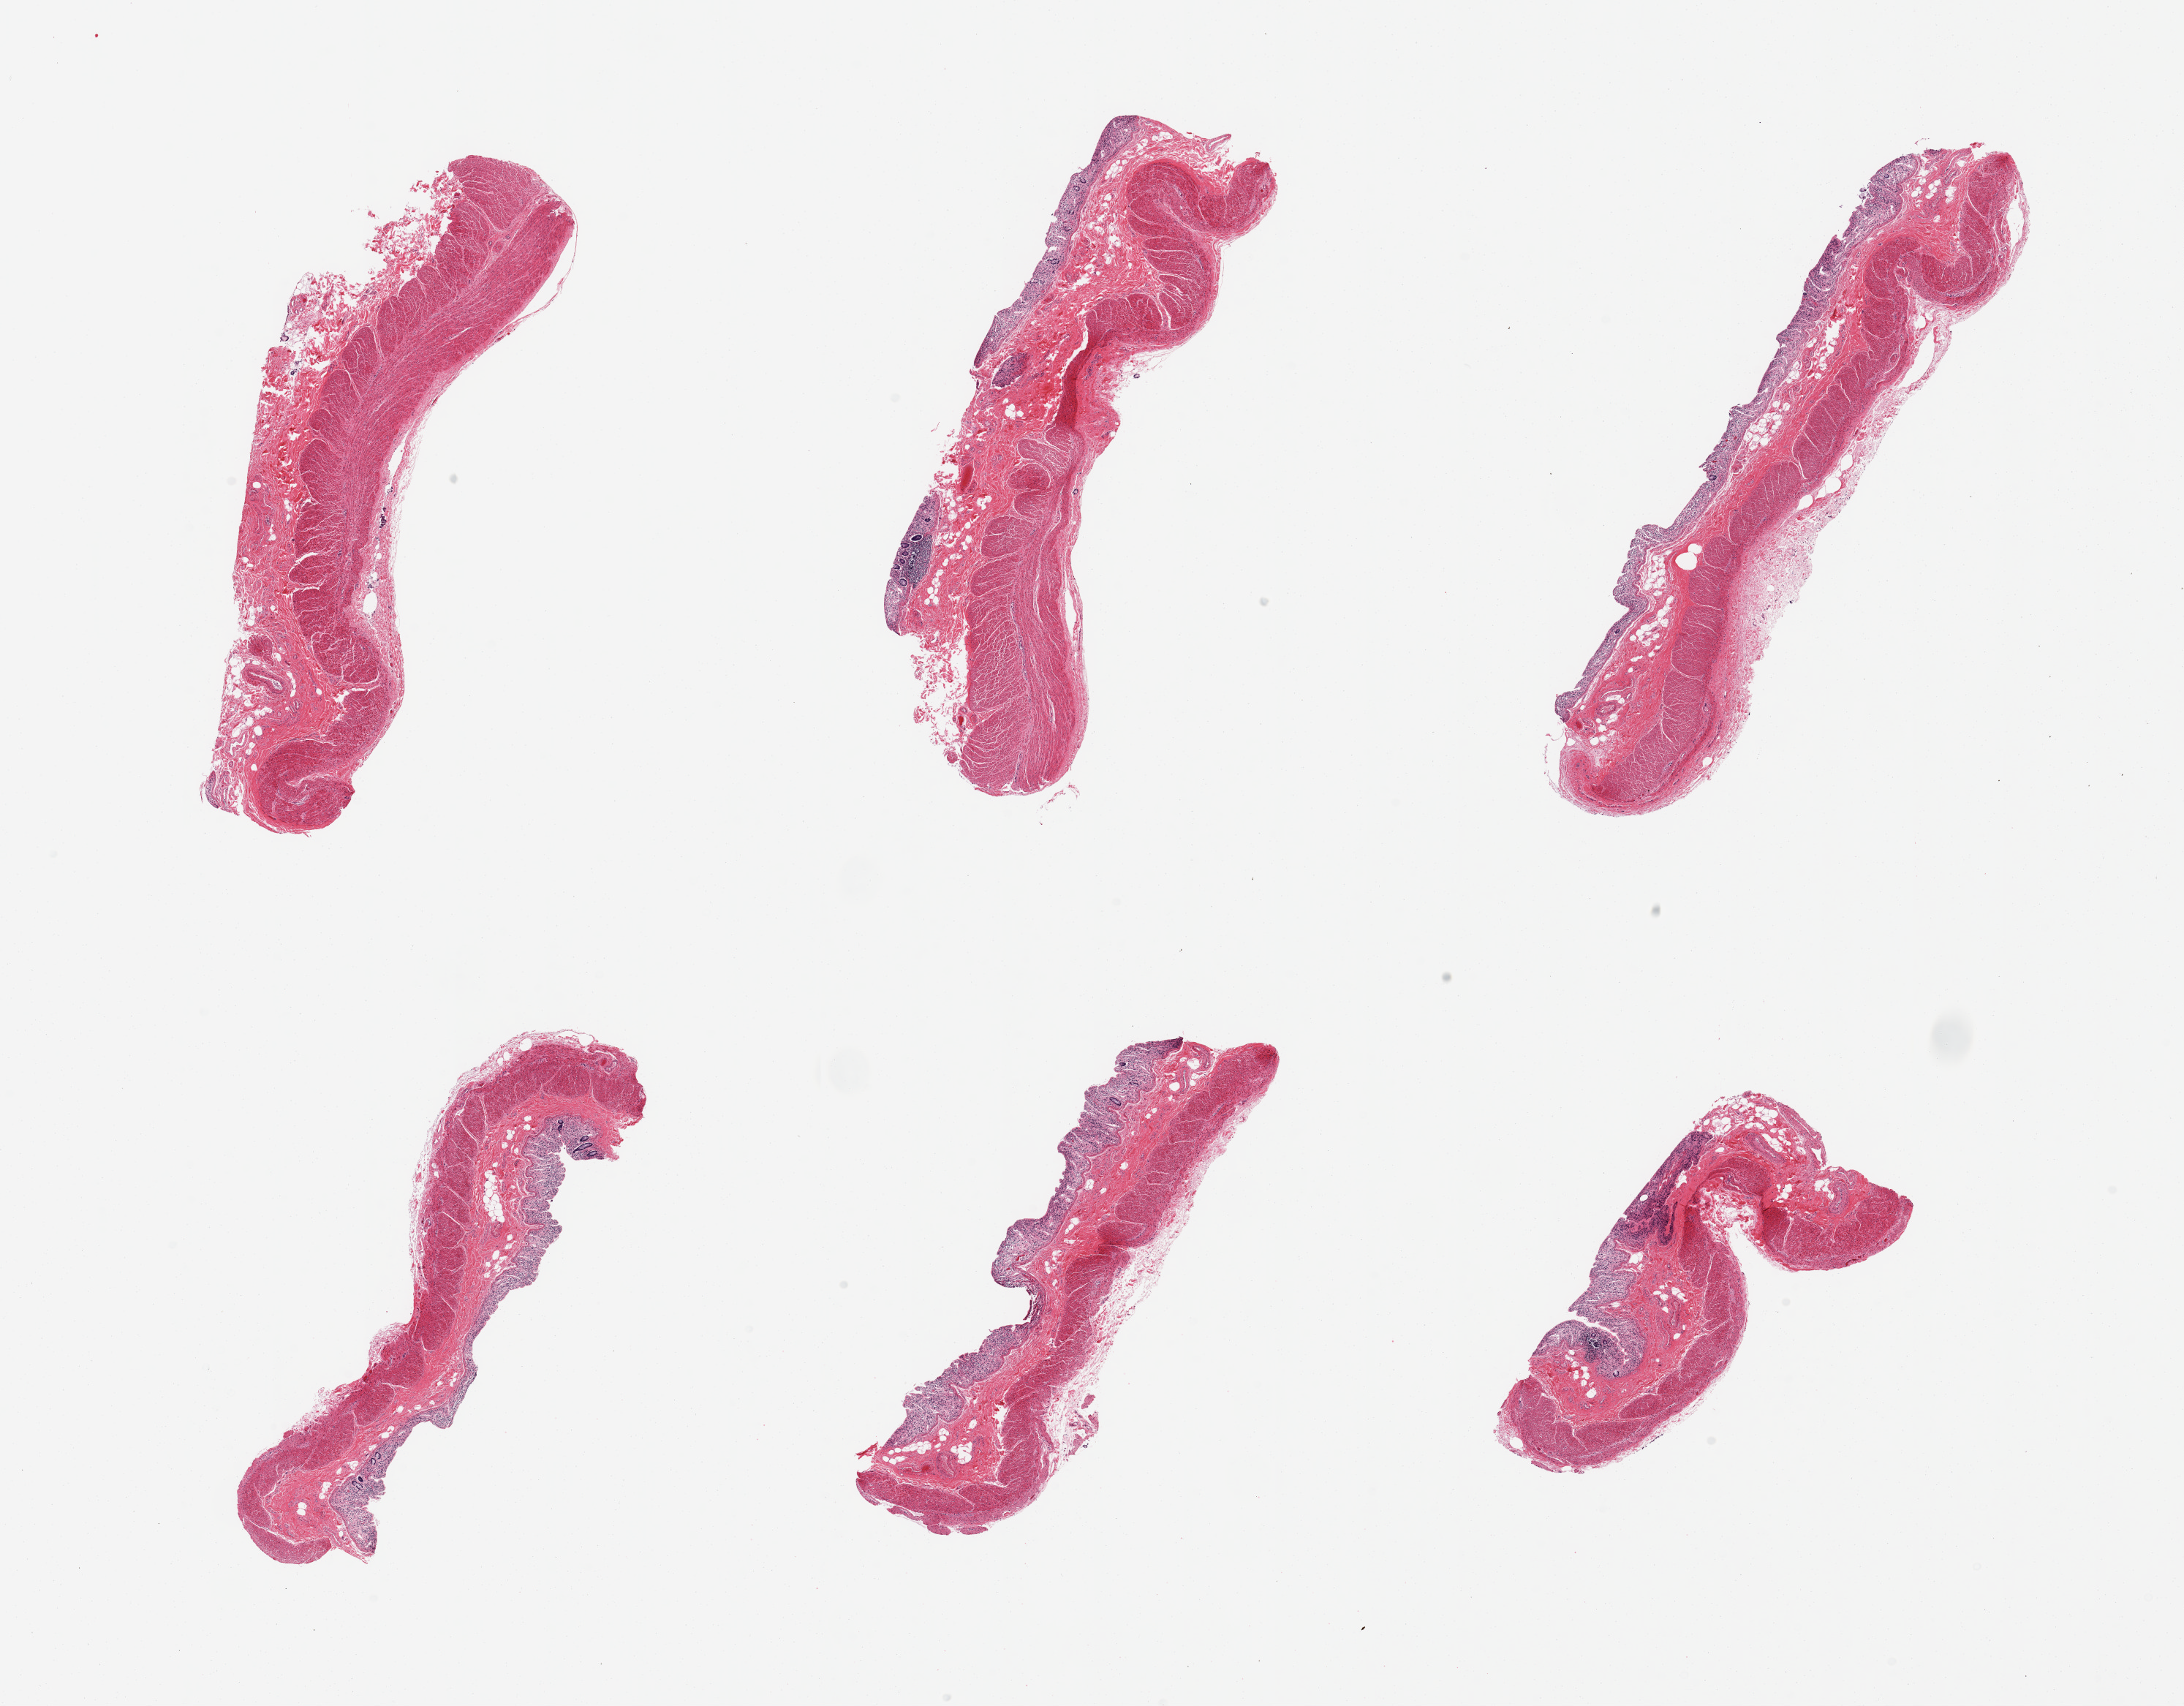
Whole-slide image, hematoxylin and eosin (H&E) stain — low-resolution overview of the scanned area, about 23.6 x 18.5 mm (slide scanned at 20x), PAXgene-fixed, paraffin-embedded tissue, section of transverse colon (target tissue), tissue donor sample. Donor: male.
Reviewer comment on this tissue sample: 6 pieces; autolyzed mucosa, intact muscularis.